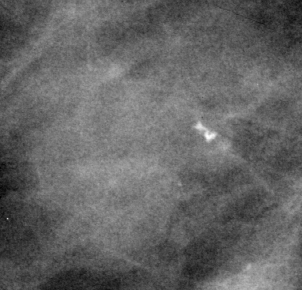
Region of interest cut from a scanned film mammogram (one marked finding); right breast; MLO view.
Finding: mass, shape lobulated, margins obscured / ill defined; BI-RADS assessment category 3; pathology (as recorded): malignant.